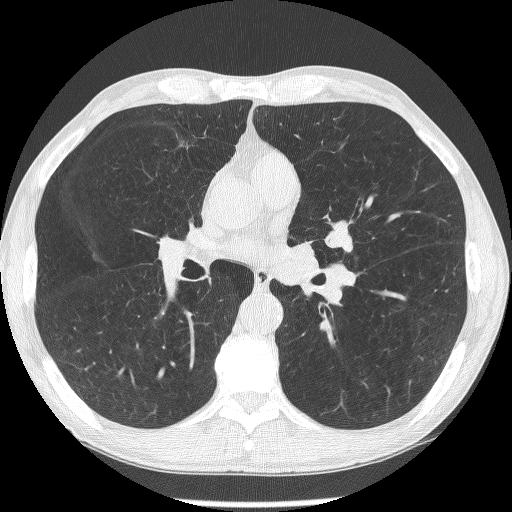
Low-dose screening chest CT, axial slice, second annual screen, lung window (W 1500 / L -600 HU), 120 kVp, slice 145 of 293 in the series. Male, age 62 years at enrolment. Former smoker at enrolment.
- Lesion marked by an expert reader, box from (x=318, y=217) to (x=368, y=265) px.
- The screening reader recorded 2 non-calcified nodules or masses ≥4 mm on this exam (lingula, lingula); which of them this box marks is not recorded.